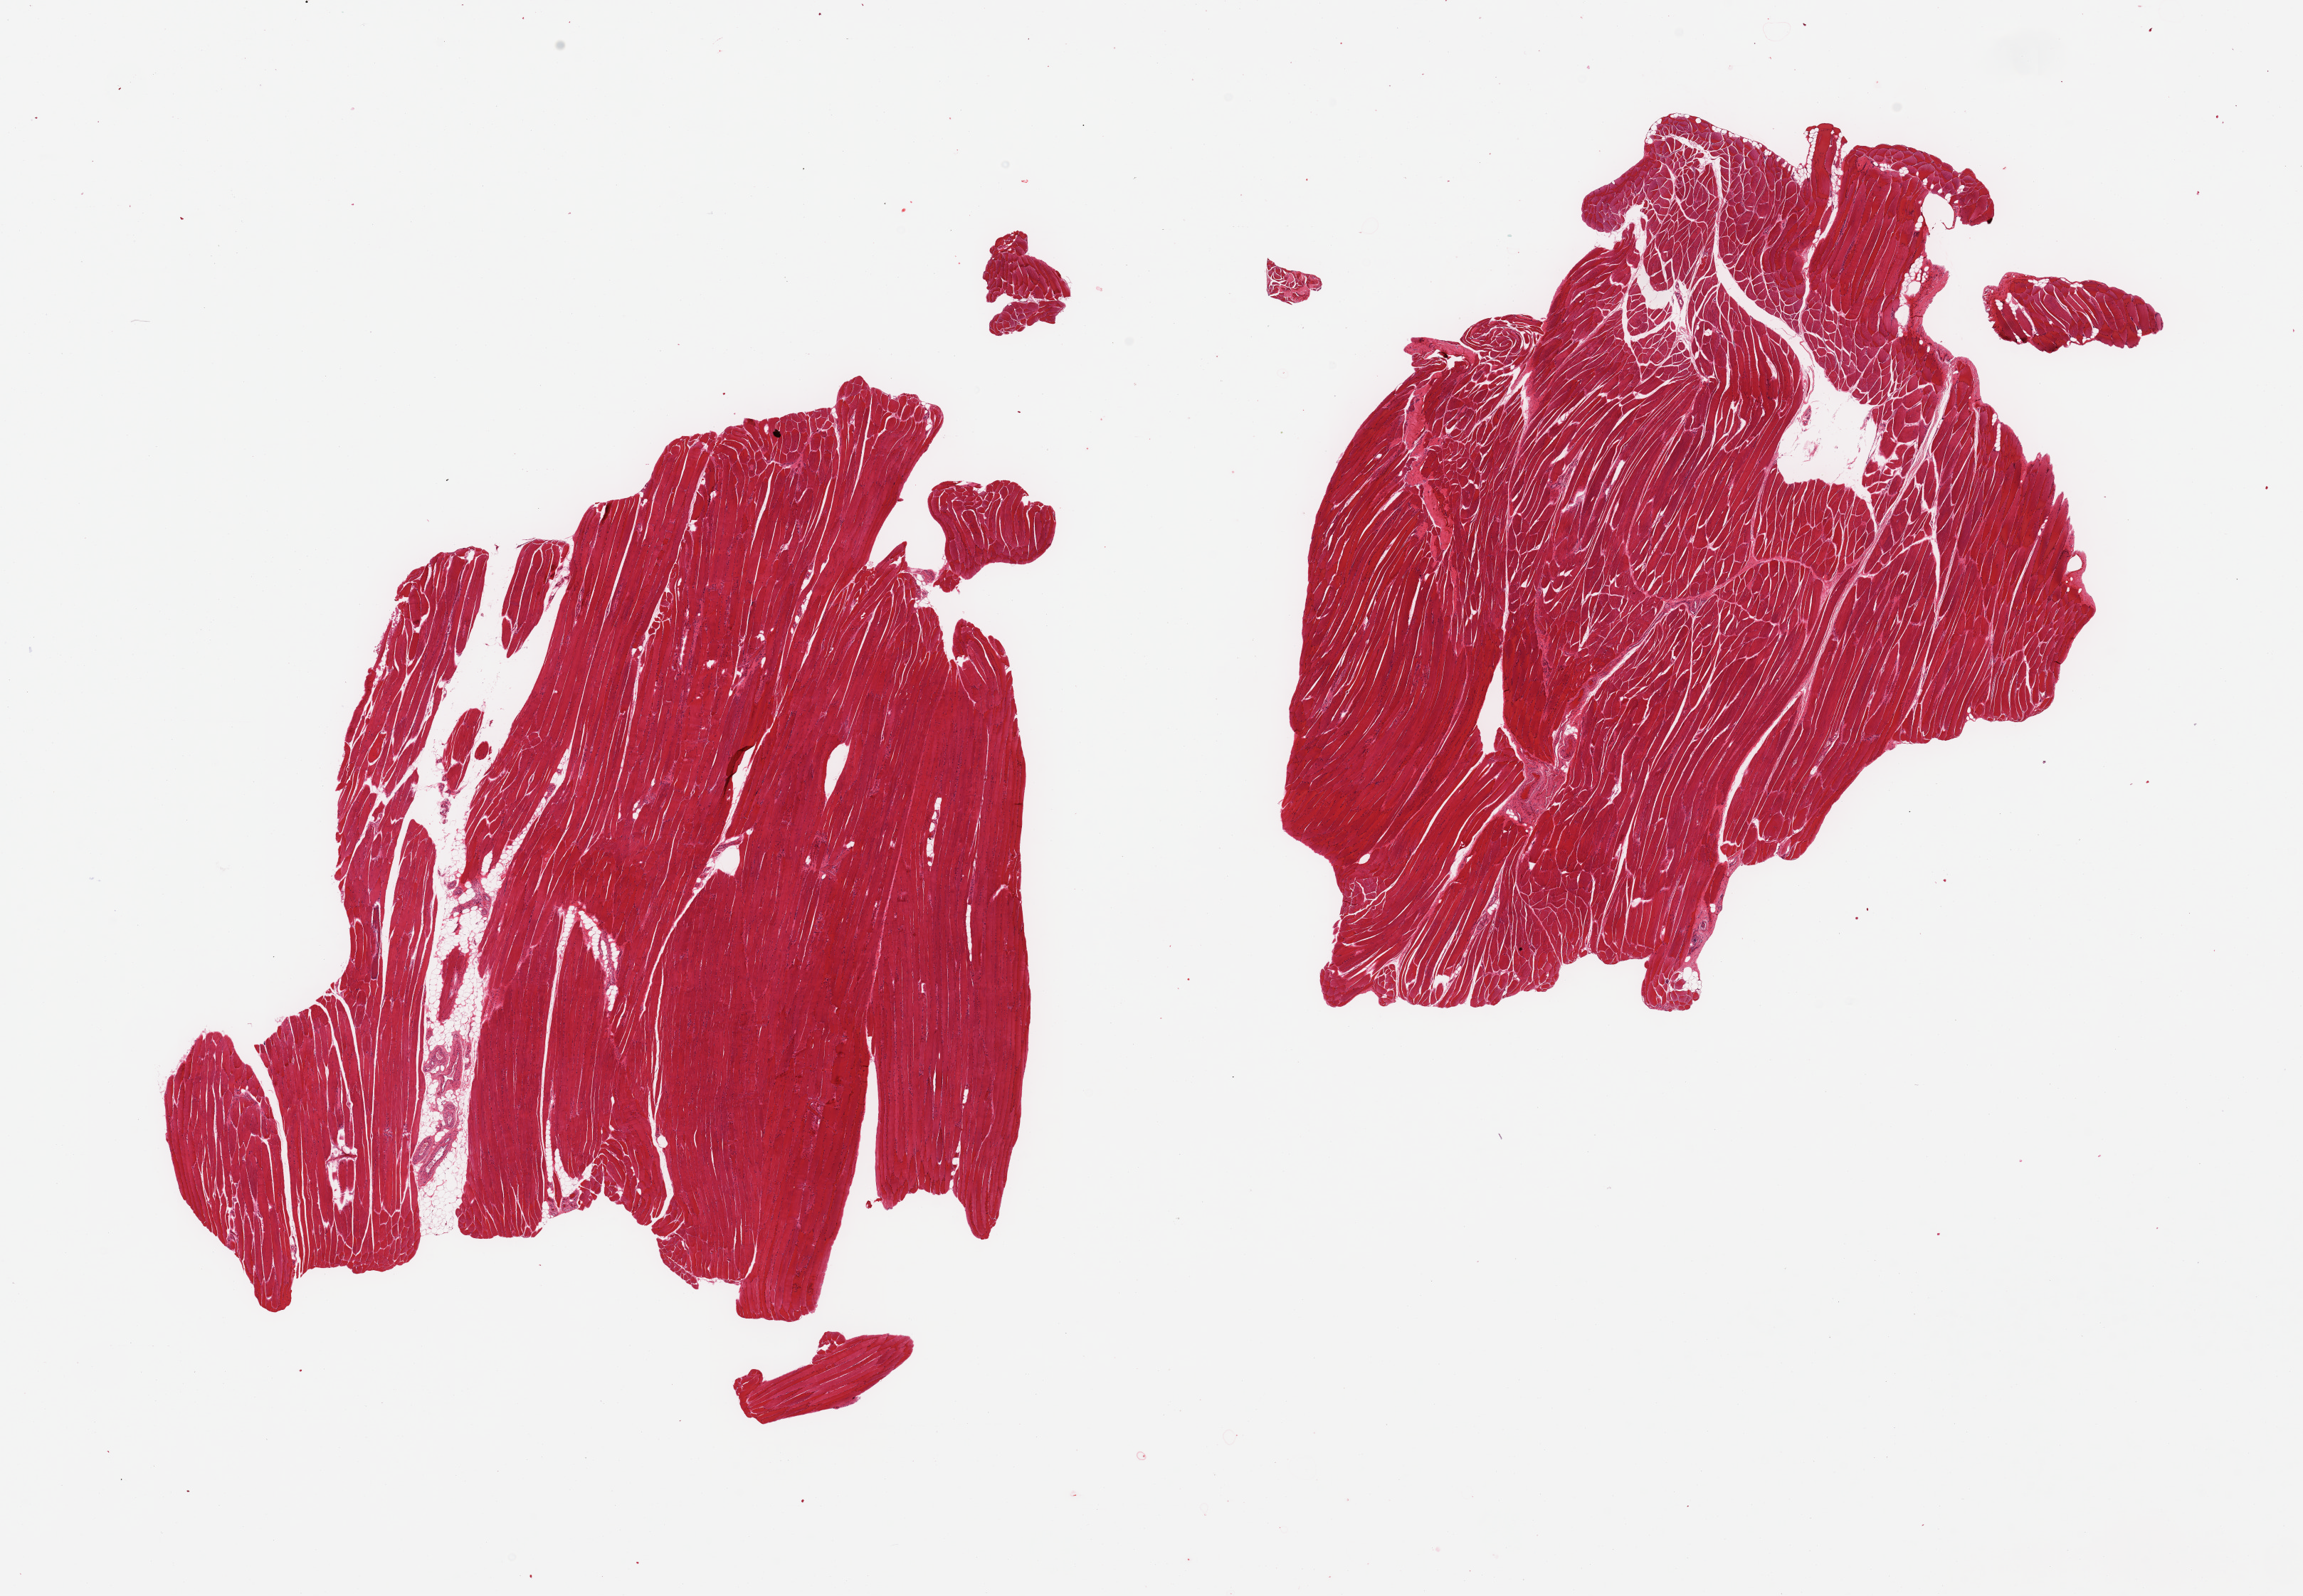
Digitized H&E-stained section, a low-resolution overview of the entire scanned area, about 25.6 x 17.7 mm. PAXgene-fixed, paraffin-embedded tissue. Sampled site (target tissue): skeletal muscle. Donor tissue sample. Donor: male.
Pathologist's review note for this sample: 2 pieces, ~5% interstitial fat.